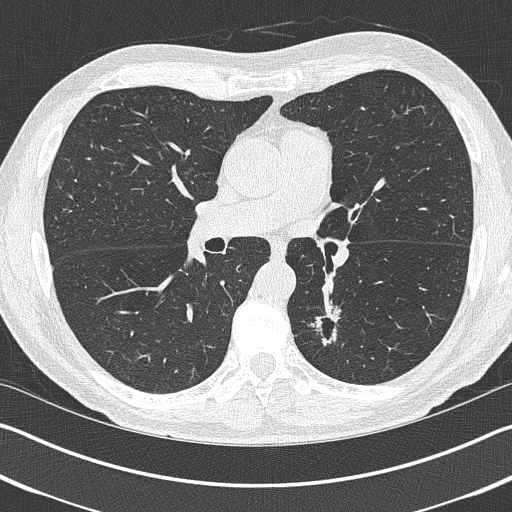
Low-dose screening chest CT, one axial slice. Position 230 of 402 along the scan axis. Reconstruction kernel B50f. 120 kVp. Lung window (W 1500 / L -600 HU). 1 mm slice thickness. 512 × 512 image matrix.
Annotated regions visible in this slice (outlined manually by an expert reader):
- lesion 1 (tumor, lower lobe of left lung): bounding box <312,301,340,346> (left, top, right, bottom; pixels)